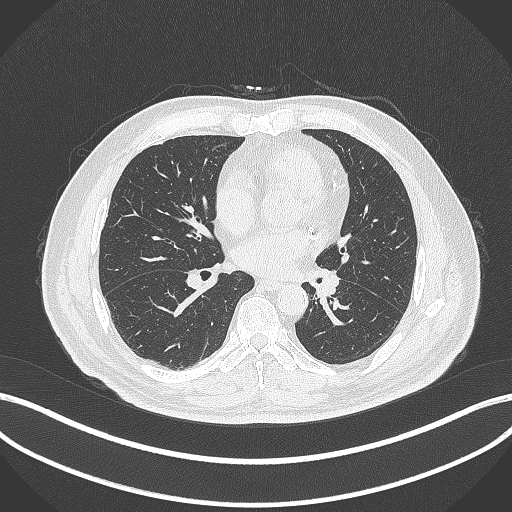
Chest CT, one axial slice; slice 130 of 312 in the series (ordered by position); lung window (W 1500 / L -600 HU); 1 mm slice thickness; 512 × 512 image matrix. Male patient, age 71 years. Case-level facts recorded for this patient, not image findings: clinical TNM (as recorded): T1b N0 M0.
Structures marked on this image (bounding box drawn by a radiologist):
- lung tumour (recorded histology: squamous cell carcinoma): bounding box (x1, y1, x2, y2) in pixels: (313, 270, 344, 300)